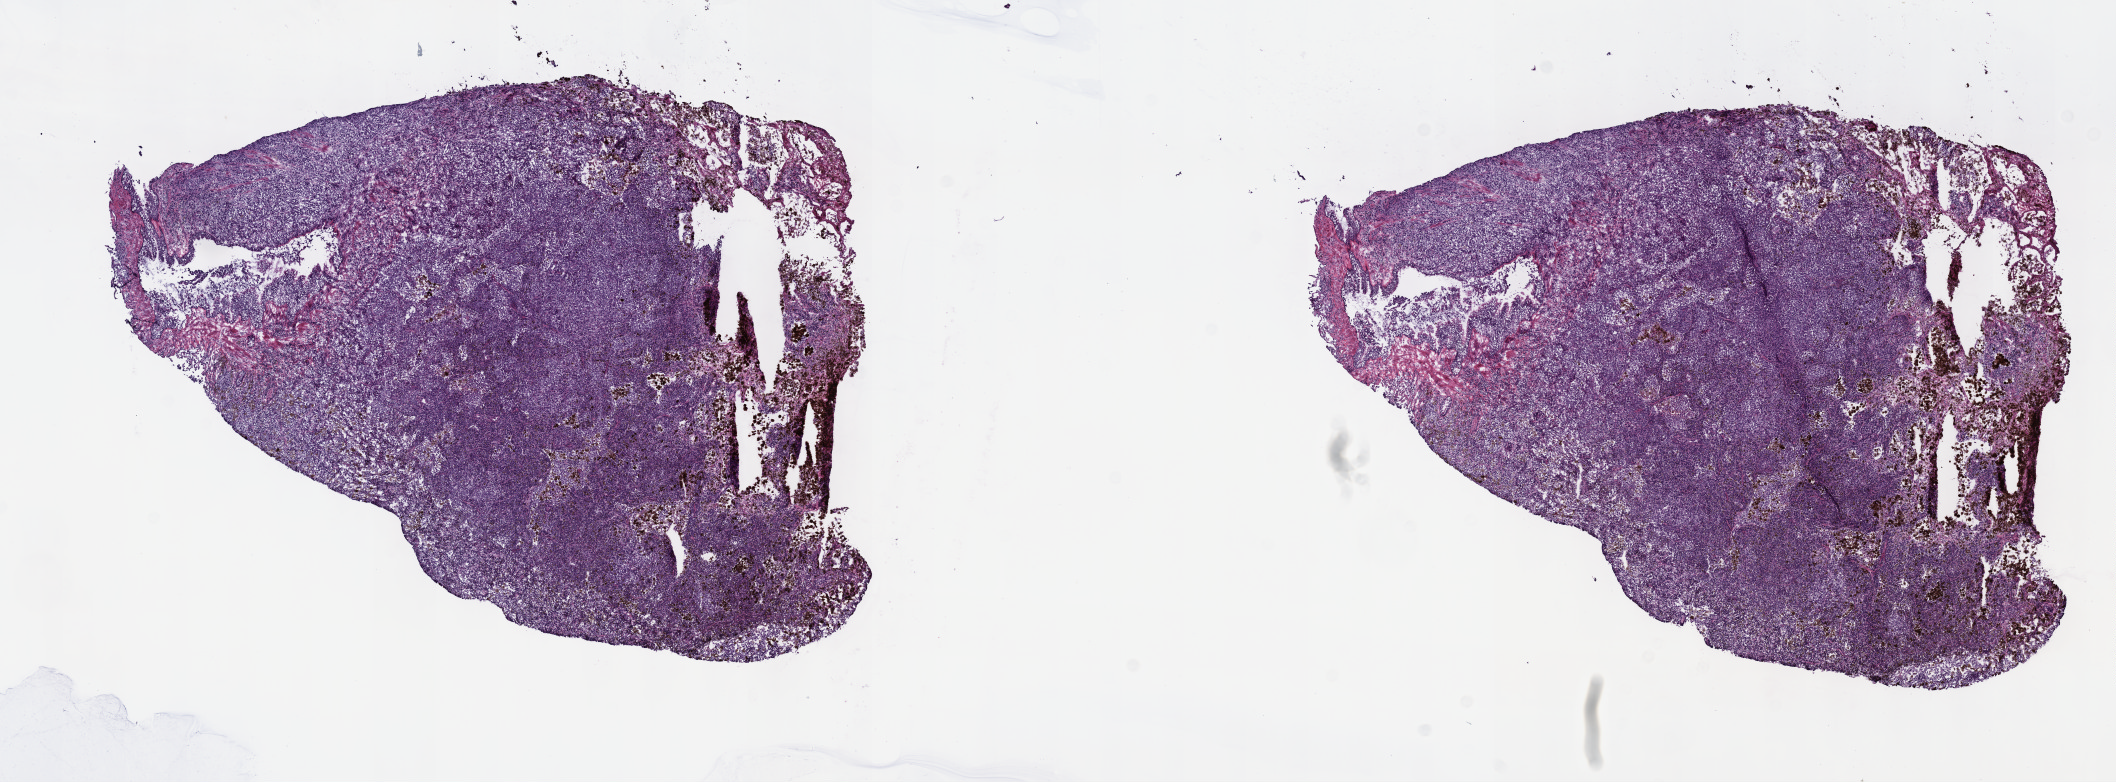
Hematoxylin and eosin (H&E) stained whole-slide image, low-resolution overview of the scanned area, about 17.1 x 6.3 mm, frozen section from the top of the tissue portion, metastatic tumour sample, sampled site: lower lobe, lung. Patient: female, age at initial diagnosis 56 years. Pathologist review of this section (percent, as recorded): tumour cells 90%, tumour nuclei 95%, normal cells 0%, stromal cells 10%, necrosis 0%. Inflammatory infiltration, as recorded: lymphocyte infiltration 0%, monocyte infiltration 0%, neutrophil infiltration 0%.
This section: metastatic tumour tissue. Patient diagnosis: Malignant melanoma, NOS.